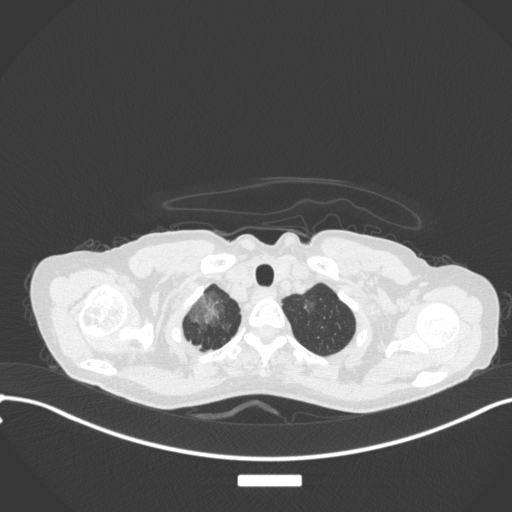
Chest CT, one axial slice. Slice 305 of 311 in the series (ordered by position). Reconstruction kernel B31f. 120 kVp. Lung window (W 1500 / L -600 HU). 1 mm slice thickness. 512 × 512 image matrix. Female patient, age 59 years. From the clinical record (not read from this slice): clinical TNM (as recorded): T3 N0 M0.
Annotated regions visible in this slice (rectangle marked by the reading radiologist):
- lung tumour (recorded histology: adenocarcinoma): bounding box <186,290,224,328> (left, top, right, bottom; pixels)